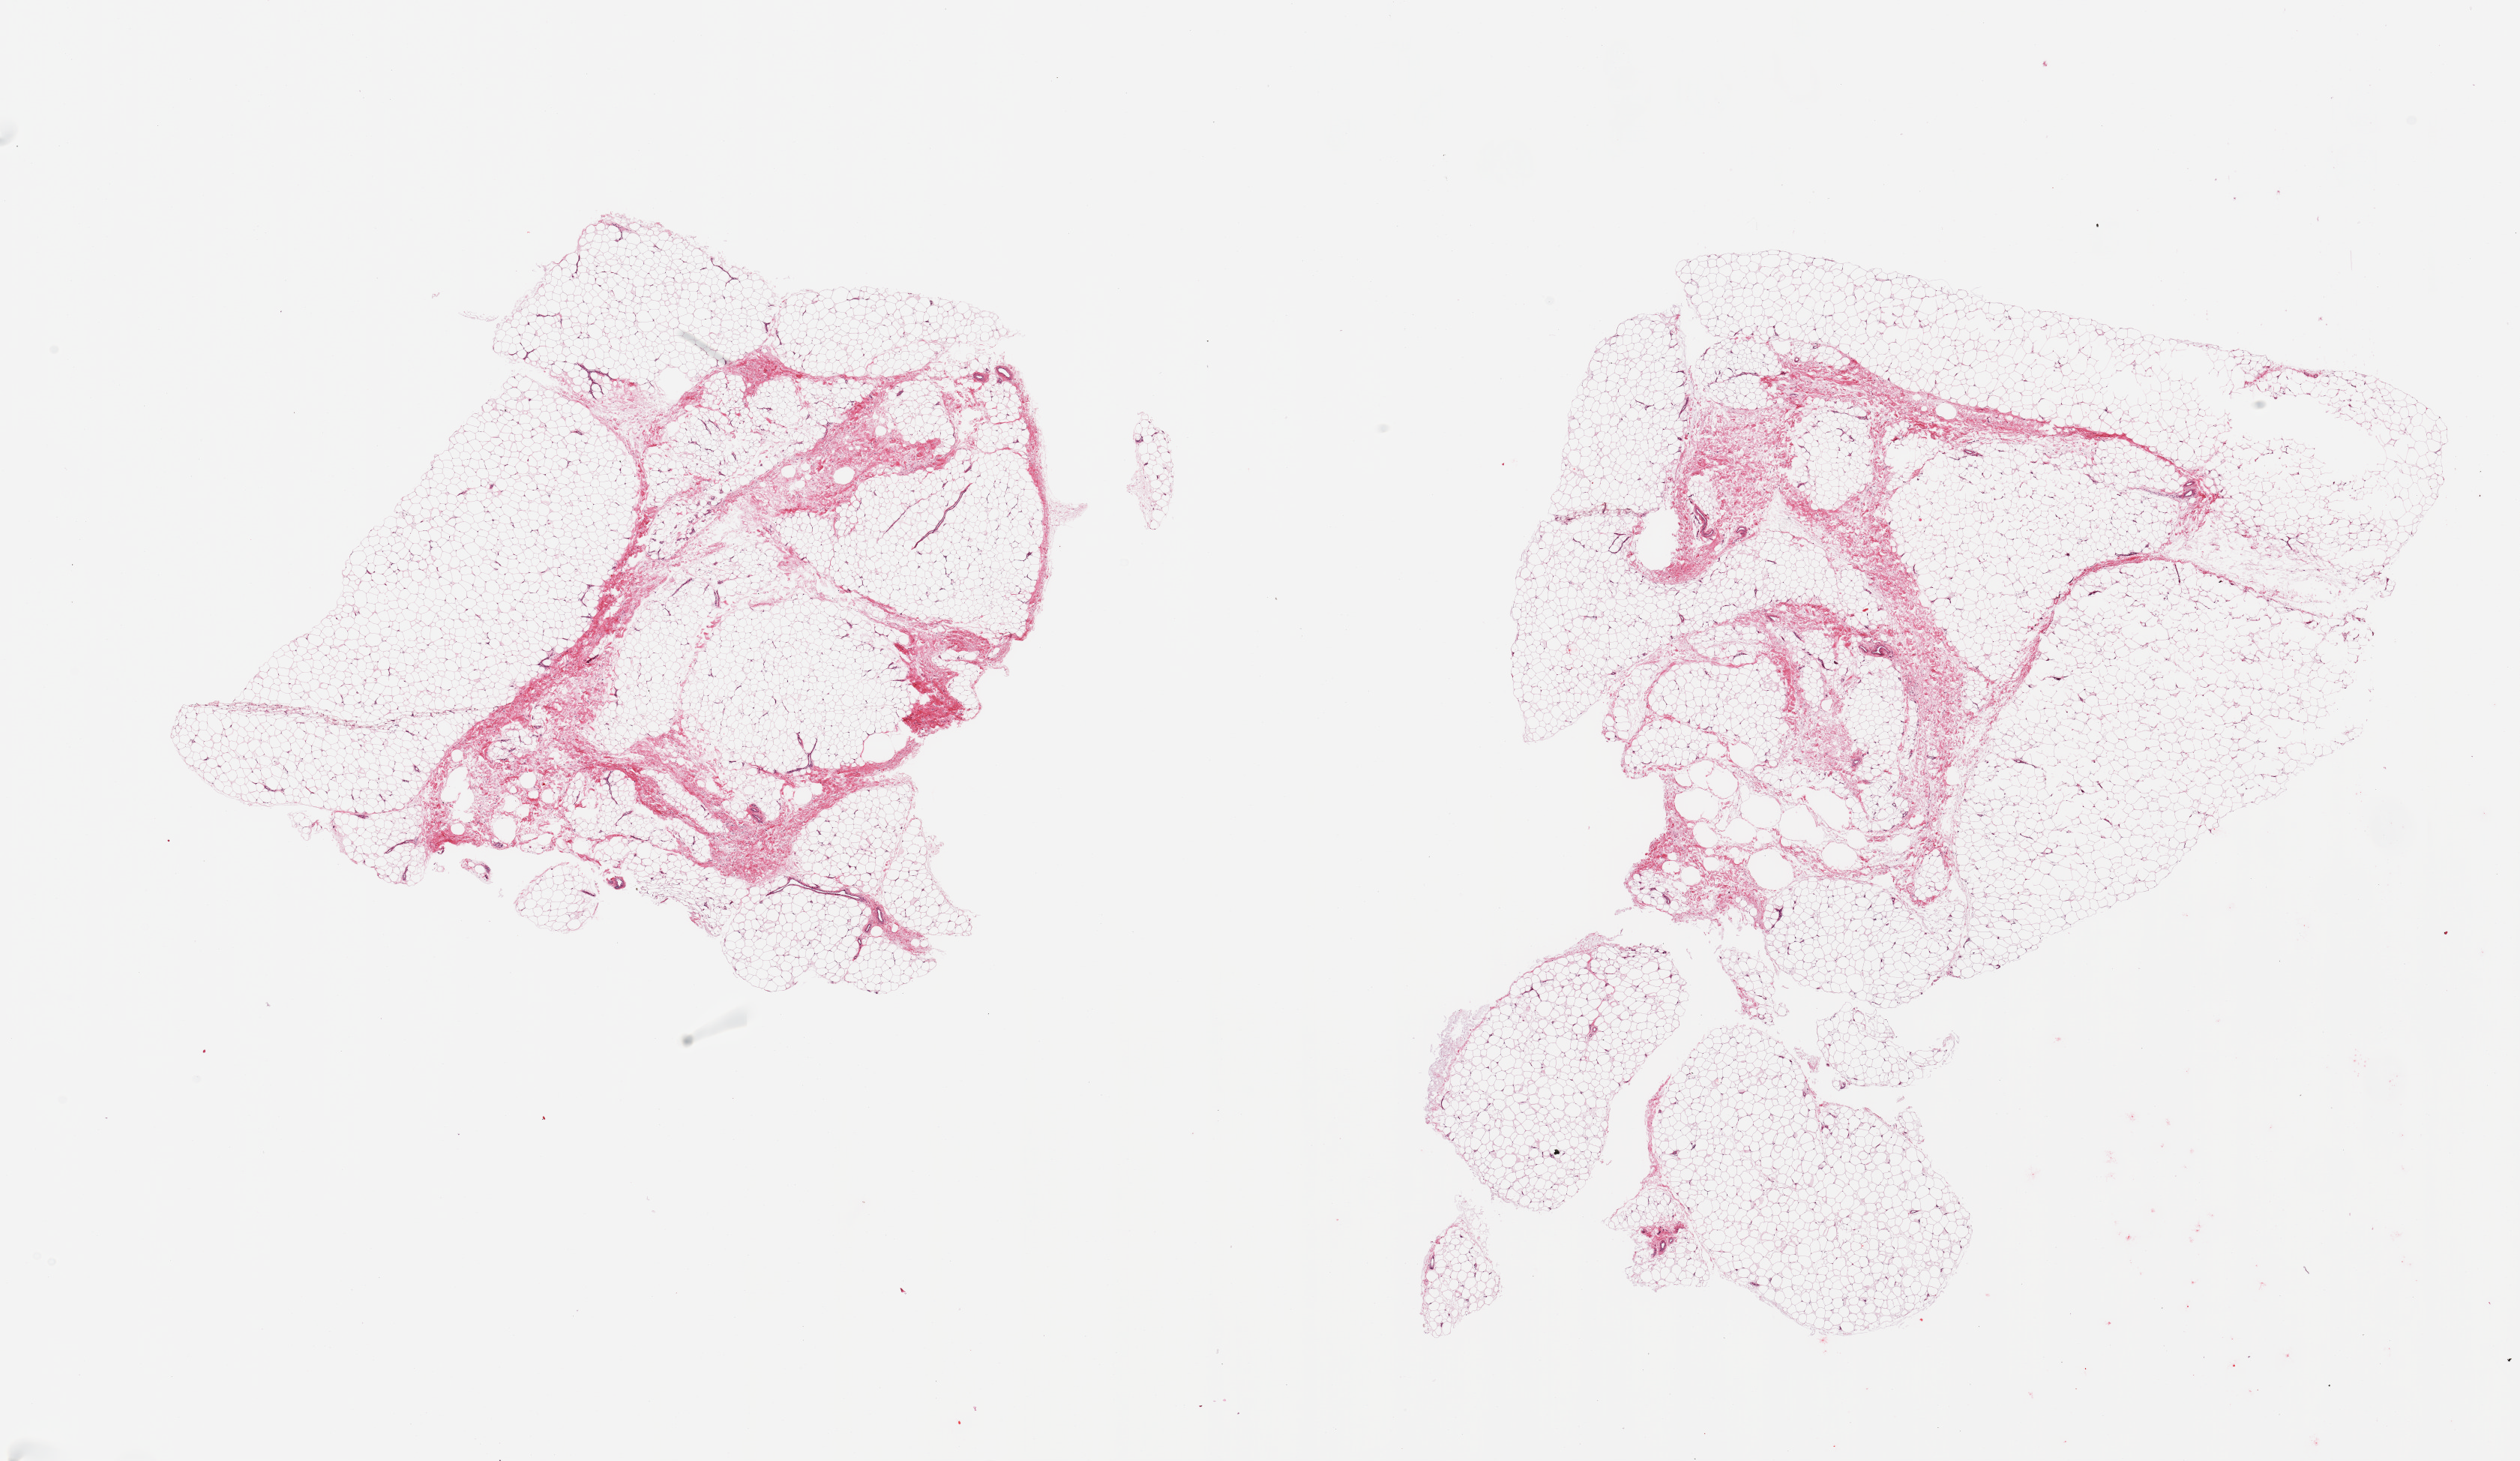
Digitized hematoxylin and eosin (H&E)-stained section, low-resolution overview of the scanned area, about 26.6 x 15.4 mm (from a 20x scan). PAXgene-fixed paraffin-embedded (PFPE) section. Target tissue: adipose tissue. Donor tissue sample. Donor: male.
• pathologist's review note for this sample: 2 pieces; mature fat with ~5-10% fibrous tissue